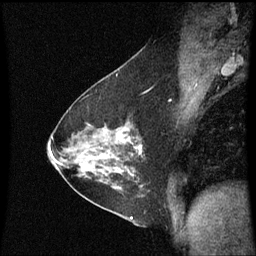
Breast MRI (dynamic contrast-enhanced), one sagittal slice; slice 37 of 60 in the series (ordered by position); dynamic contrast-enhanced series, image 2 of 3 at this slice position (ordered by acquisition); 1.5 T; TE 4.2 ms, TR 8.9 ms; 2 mm slice thickness; 256 × 256 image matrix, field of view 200 × 200 mm. Patient: female, 54 years. Case-level facts recorded for this patient, not image findings: setting: breast cancer imaged before/during neoadjuvant chemotherapy; receptor status: HER2-positive.
Annotated regions visible in this slice (semi-automatic segmentation, software-assisted and operator-edited):
- analysis volume of interest (the breast-tissue region the enhancement analysis was run in; not a lesion): box from (x=102, y=122) to (x=145, y=169) px
- tumour enhancement mask (voxels above the 70 % enhancement threshold inside the analysis volume of interest): (x=116, y=134)–(x=142, y=153)